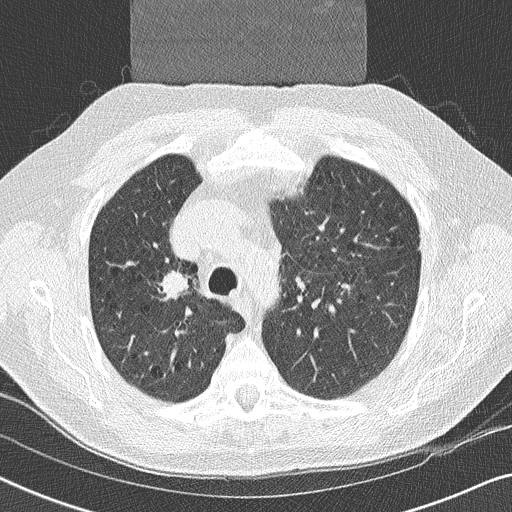
Axial slice from a low-dose chest CT screening exam, second annual screen, lung window (W 1500 / L -600 HU), 2 mm slice thickness, lung (sharp) reconstruction kernel (B50f). Male participant, aged 59 years at enrolment. Former smoker at enrolment.
Lesion marked by an expert reader, bounding box <145,257,204,308> (left, top, right, bottom; pixels). Screening reader's record for this exam (one nodule recorded; not confirmed to be the boxed lesion): non-calcified nodule or mass ≥4 mm, right upper lobe, 17 × 16 mm, smooth margins, soft tissue attenuation, pre-existing on the prior screen: yes. Later outcome: lung cancer diagnosed 14 days after this screen — squamous cell carcinoma, NOS, right upper lobe, poorly differentiated (G3), stage IIA (AJCC 6th edition), 20 mm at pathology.